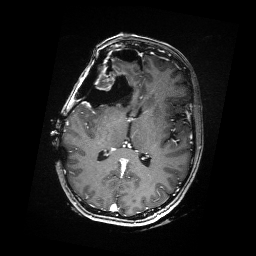
Brain MRI from a brain-tumour surgery series, one axial slice. Slice 88 of 176 in the series (ordered by position). T1-weighted post-contrast. 256 × 256 image matrix, field of view 256 × 256 mm. Case-level facts recorded for this patient, not image findings: histopathology: Metastatic Carcinoma from Breast primary; tumour location: Right Frontal.
Structures marked on this image (expert manual segmentation):
- residual tumour: bounding box (x1, y1, x2, y2) in pixels: (88, 68, 117, 89)